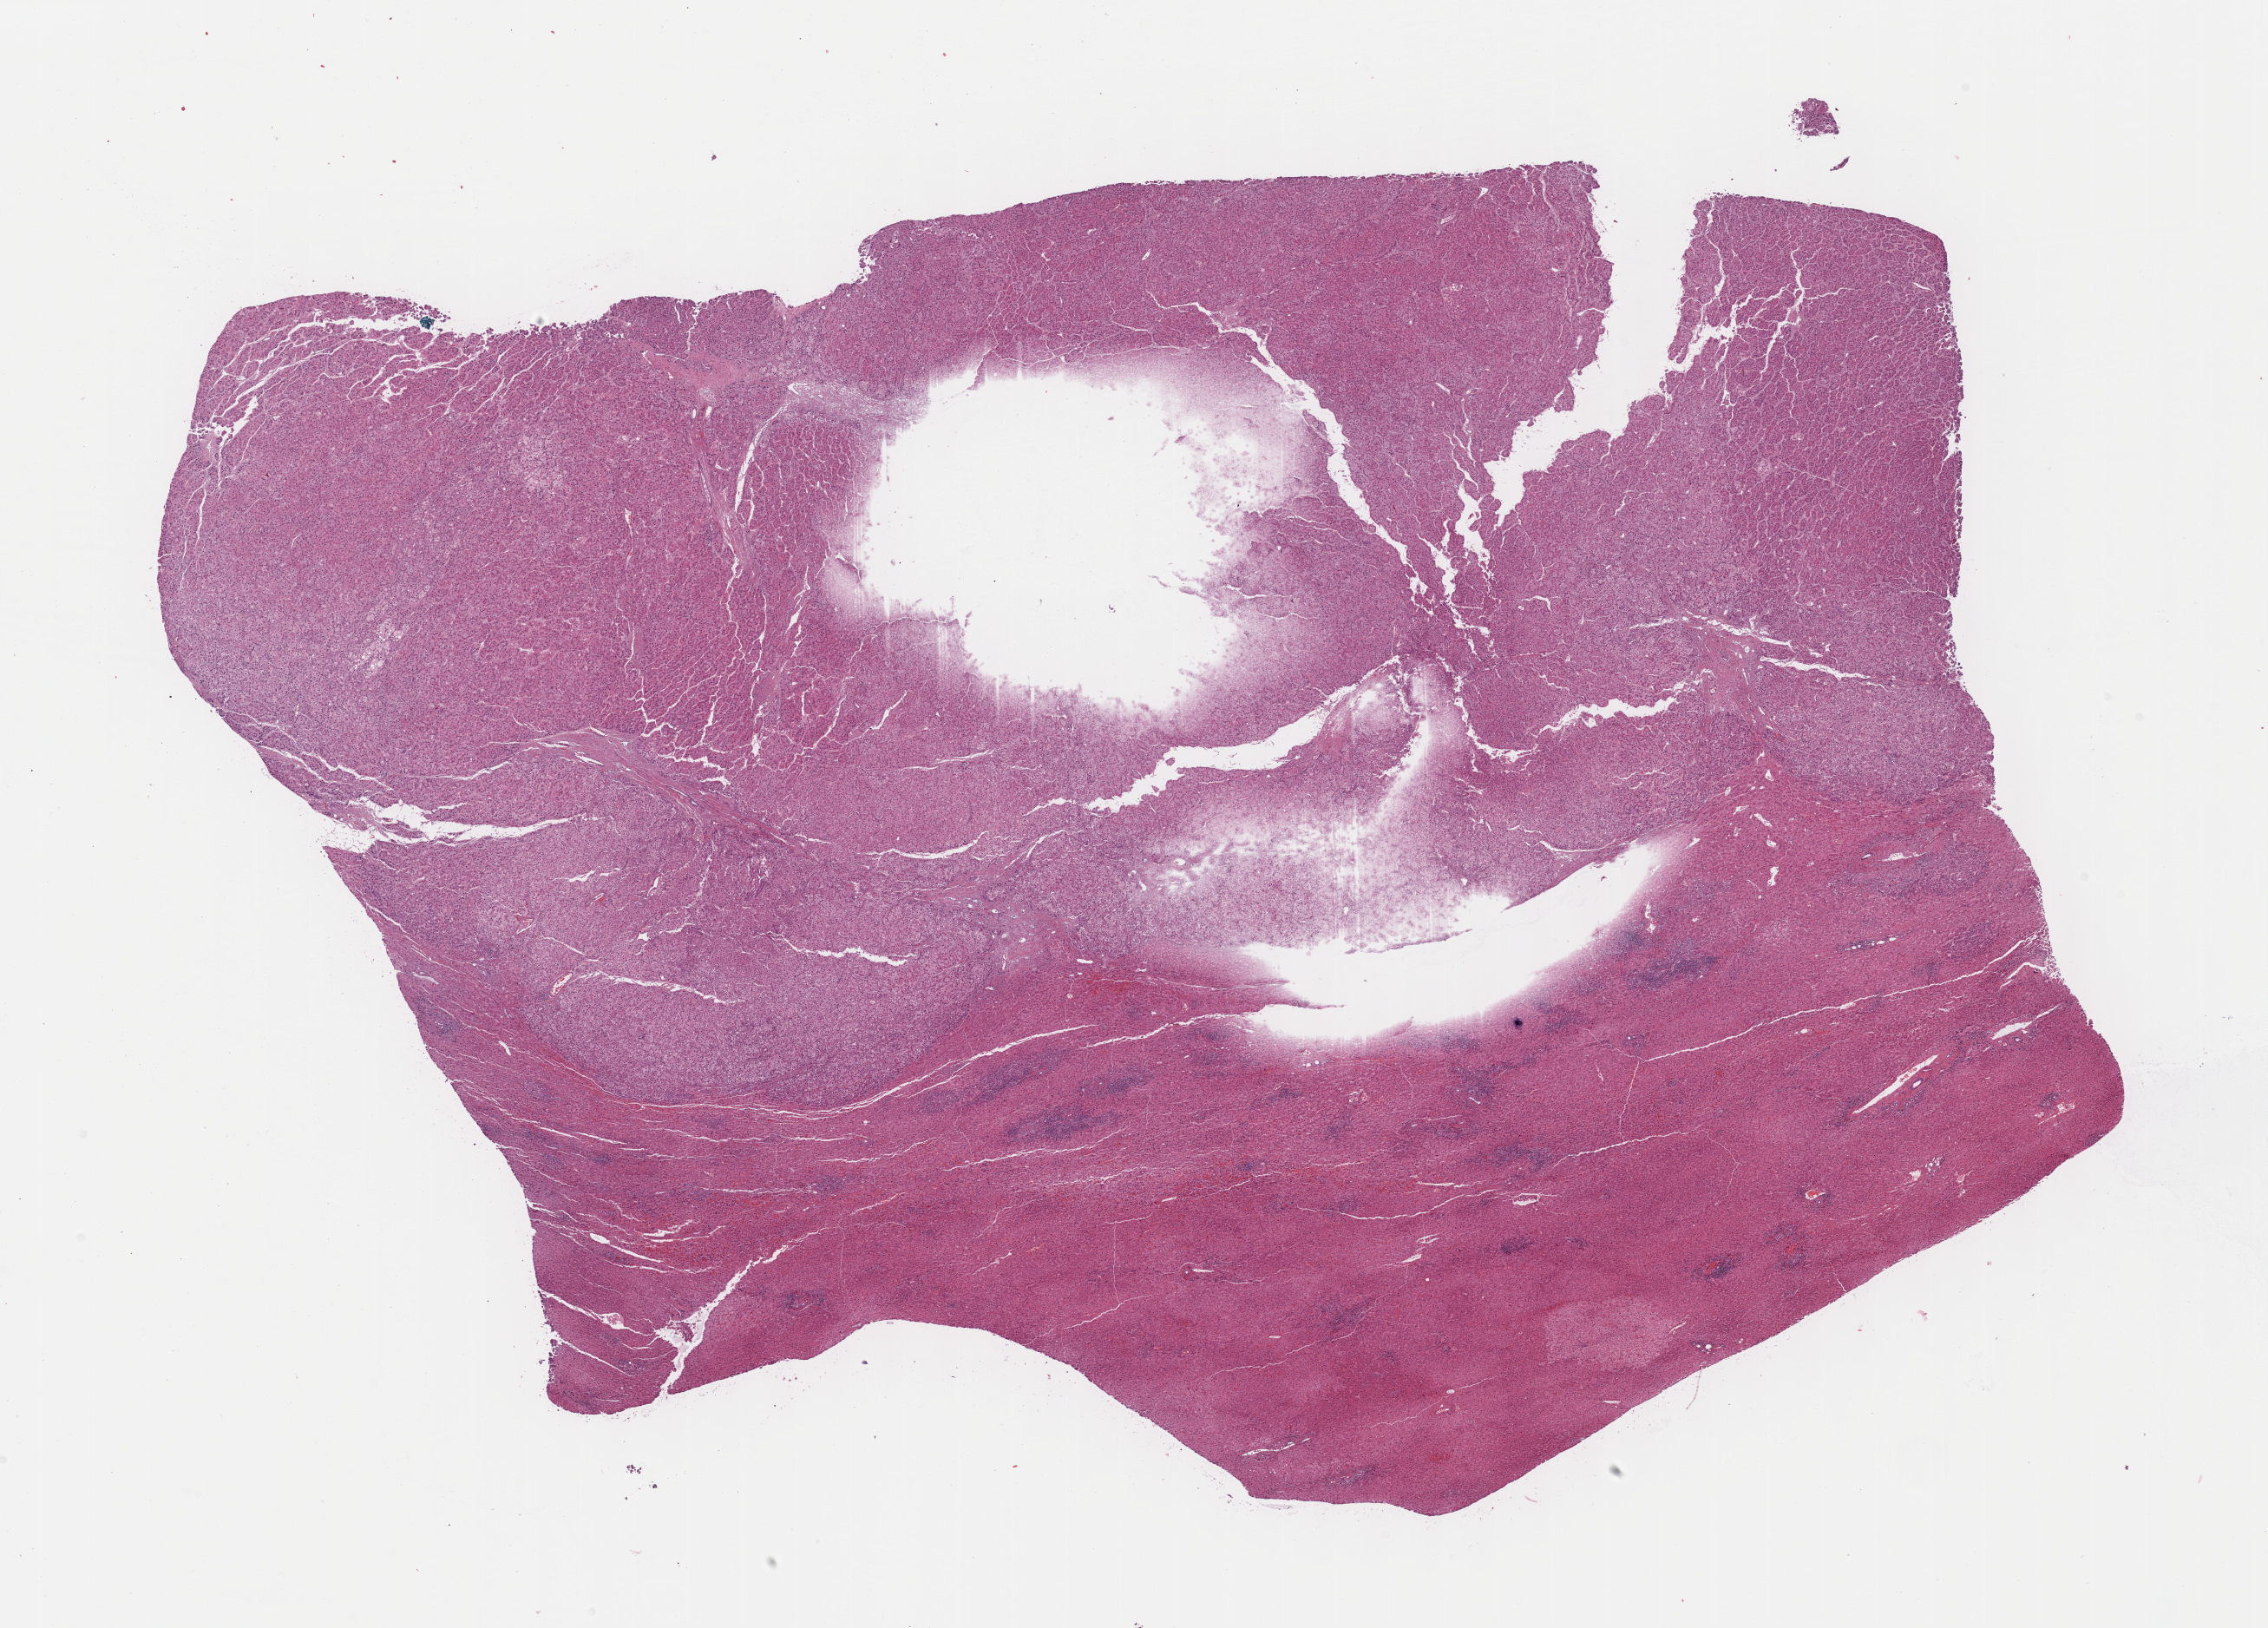
Whole-slide histology image, Hematoxylin and eosin (H&E) stained, low-resolution overview of the scanned area, about 21.1 x 15.2 mm (from a 40x scan), formalin-fixed paraffin-embedded (FFPE) diagnostic section, primary tumour sample from the liver. Patient: male, age at initial diagnosis 68 years. Histologic grade: G2 (moderately differentiated).
* pathologic diagnosis: Hepatocellular carcinoma, NOS